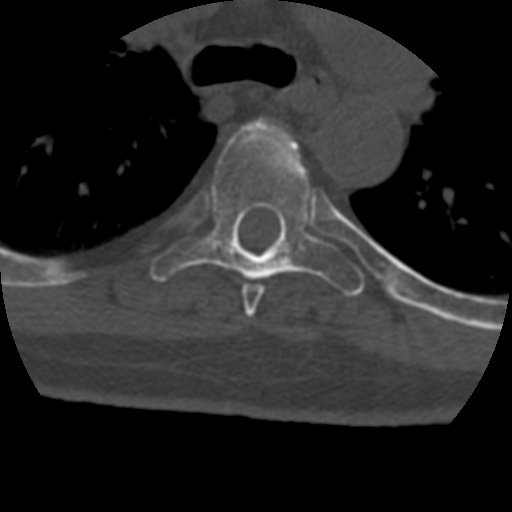
CT including the spine, one axial slice; slice 305 of 399 in the series (ordered by position); 120 kVp; bone window (W 1800 / L 400 HU); 1.25 mm slice thickness; 512 × 512 image matrix, field of view 160 × 160 mm. Patient age 69 years. From the clinical record (not read from this slice): primary cancer: prostate.
Outlined on this slice (semi-automatically segmented with operator editing):
- T5 vertebra: box from (x=242, y=141) to (x=296, y=319) px
- T6 vertebra: (x=151, y=120)–(x=365, y=296)